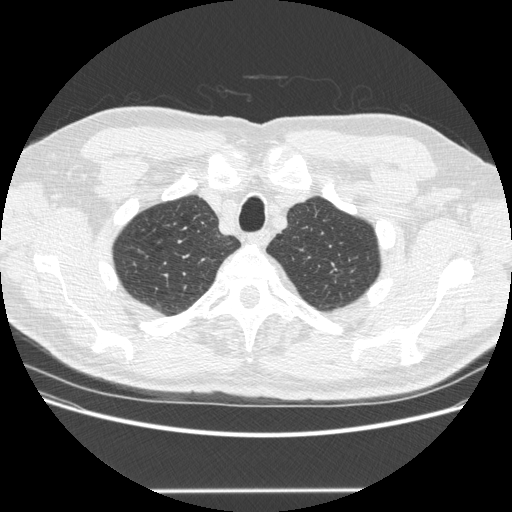
Chest CT (low-dose screening protocol), one axial image; second annual screen; lung window (W 1500 / L -600 HU); 1.25 mm slice thickness; standard (soft-tissue) reconstruction kernel (STANDARD); 512 × 512 image matrix. Male participant, aged 69 years at enrolment. Former smoker at enrolment.
Lesion marked by an expert reader, bounding box <310,260,348,294> (left, top, right, bottom; pixels). Screening reader's record for this exam: no non-calcified nodule ≥4 mm recorded. Lung cancer was diagnosed 485 days after this screen: adenocarcinoma, NOS, left upper lobe, moderately differentiated (G2), stage IA (AJCC 6th edition), 10 mm at pathology.